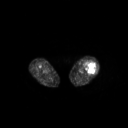
FDG PET of an extremity soft-tissue mass (from a PET/CT study), one axial slice. Position 201 of 267 along the scan axis. 3.27 mm slice thickness. 128 × 128 image matrix, field of view 700 × 700 mm. Patient: female, 62 years. From the clinical record (not read from this slice): histological type: undifferentiated – high grade; grade: high; site of the primary tumour: left thigh.
Structures marked on this image (expert contour drawn on MRI and transferred to this co-registered scan by the dataset authors):
- gross tumour volume including surrounding oedema: bounding box (x1, y1, x2, y2) in pixels: (84, 61, 96, 74)